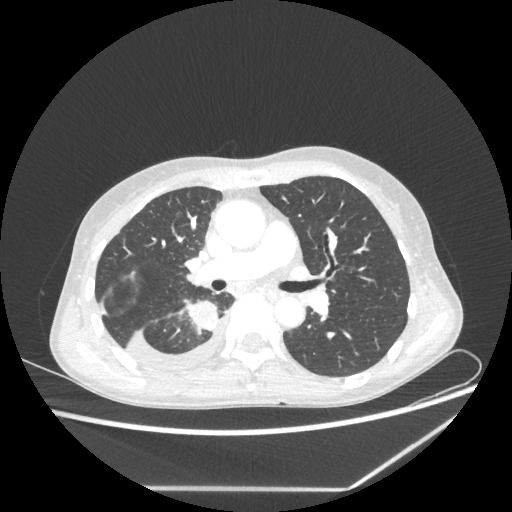
Chest CT, one axial slice; position 135 of 237 along the scan axis; lung window (W 1500 / L -600 HU); 512 × 512 image matrix, field of view 364 × 364 mm. Female patient, age 59 years. From the clinical record (not read from this slice): clinical TNM (as recorded): T1c N1 M1.
Annotated regions visible in this slice (bounding box drawn by a radiologist):
- lung tumour (recorded histology: adenocarcinoma): bounding box [x1, y1, x2, y2] px = [186, 298, 221, 338]